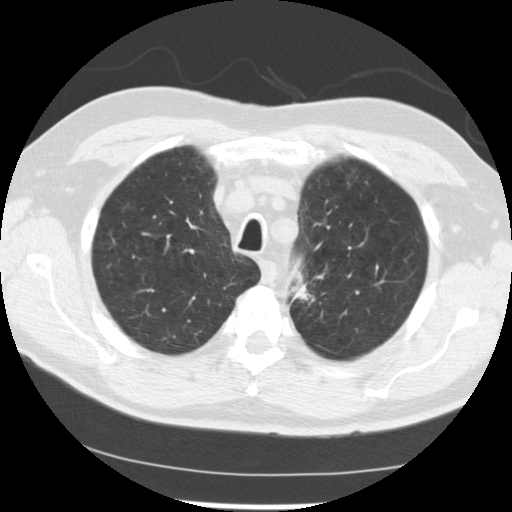
Axial slice from a low-dose chest CT screening exam, baseline annual screen, lung window (W 1500 / L -600 HU), 2.5 mm slice thickness, slice 197 of 249 in the series. Male participant, aged 71 years at enrolment. Current smoker at enrolment.
Expert-annotated lung lesion, bounding box (x1, y1, x2, y2) in pixels: (275, 258, 334, 315). The screening reader recorded 2 non-calcified nodules or masses ≥4 mm on this exam (left upper lobe, left upper lobe); which of them this box marks is not recorded. Official screen result: positive, change unspecified: nodule(s) >= 4 mm or enlarging nodule(s), mass(es), or other non-specific abnormalities suspicious for lung cancer. Lung cancer was diagnosed 37 days after this screen: adenocarcinoma, NOS, left upper lobe, poorly differentiated (G3), stage IIIB (AJCC 6th edition), 25 mm at pathology.